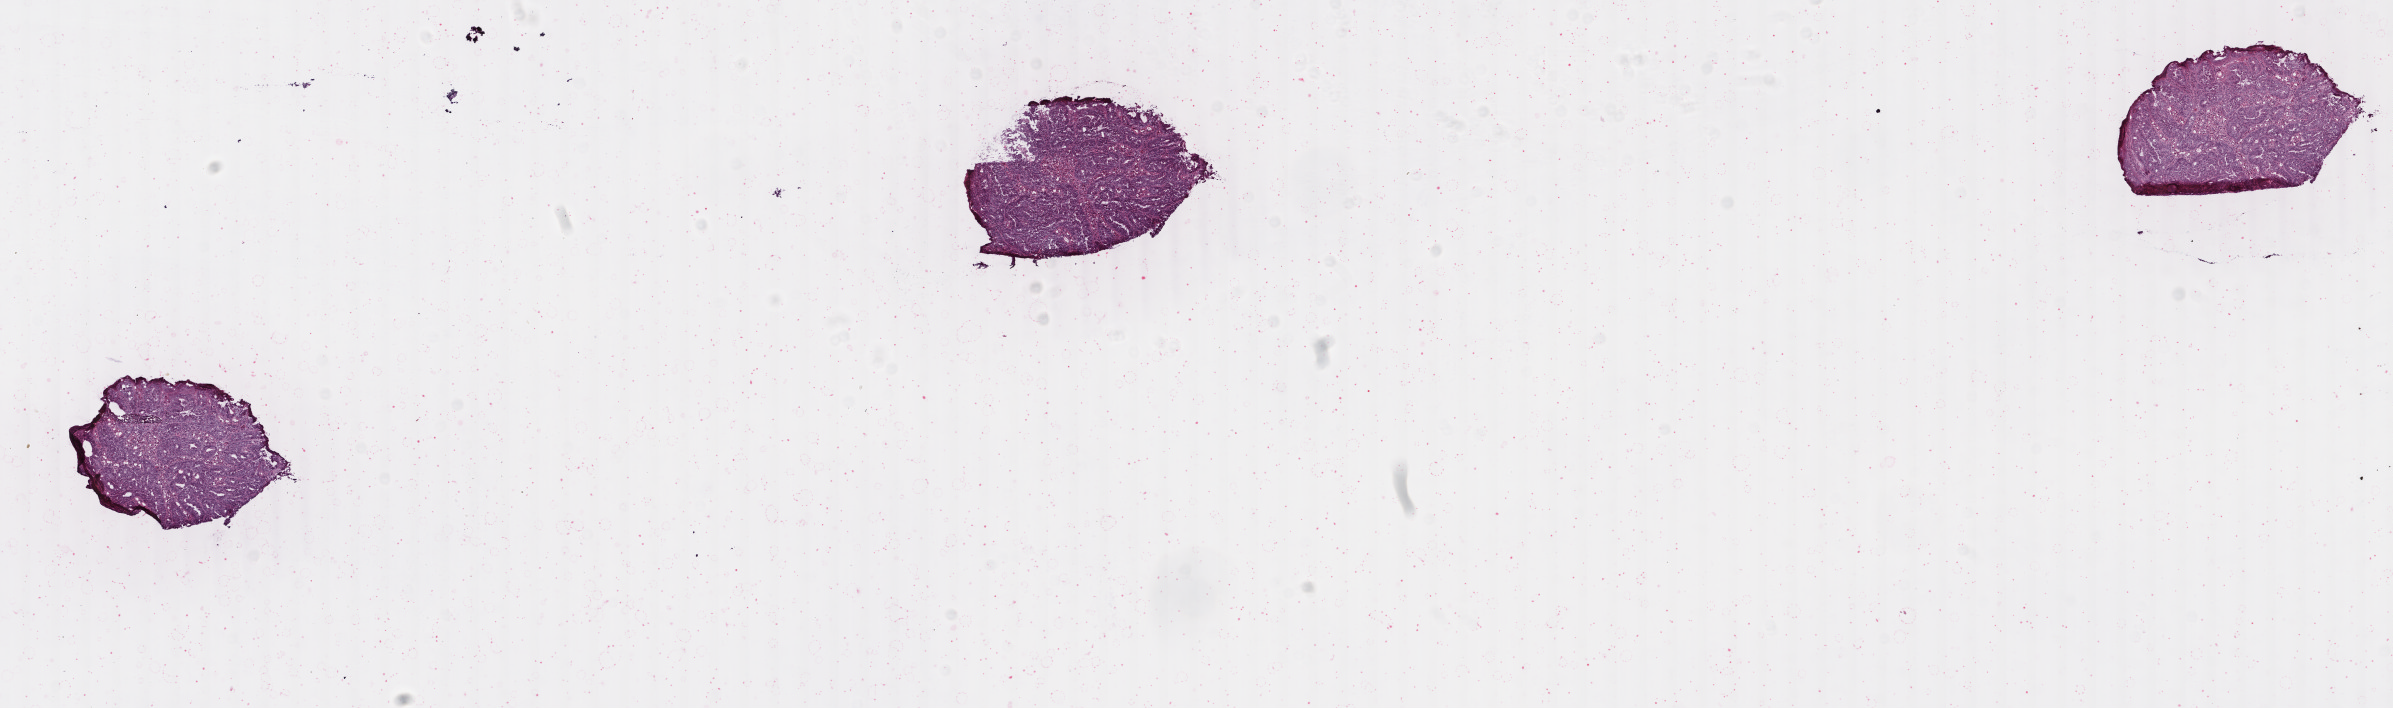
H&E whole-slide image — low-resolution overview of the scanned area, about 19.0 x 5.6 mm; frozen section from the bottom of the tissue portion; sample: primary tumour, colon. Male patient; age at initial diagnosis 76 years. Slide review estimates, as recorded: tumour cells 90%, tumour nuclei 90%, normal cells 0%, stromal cells 9%, necrosis 1%. Infiltration values recorded for this section: lymphocyte infiltration 2%, monocyte infiltration 1%, neutrophil infiltration 1%.
• AJCC pathologic stage: I
• diagnosis: Adenocarcinoma, NOS (sigmoid colon)